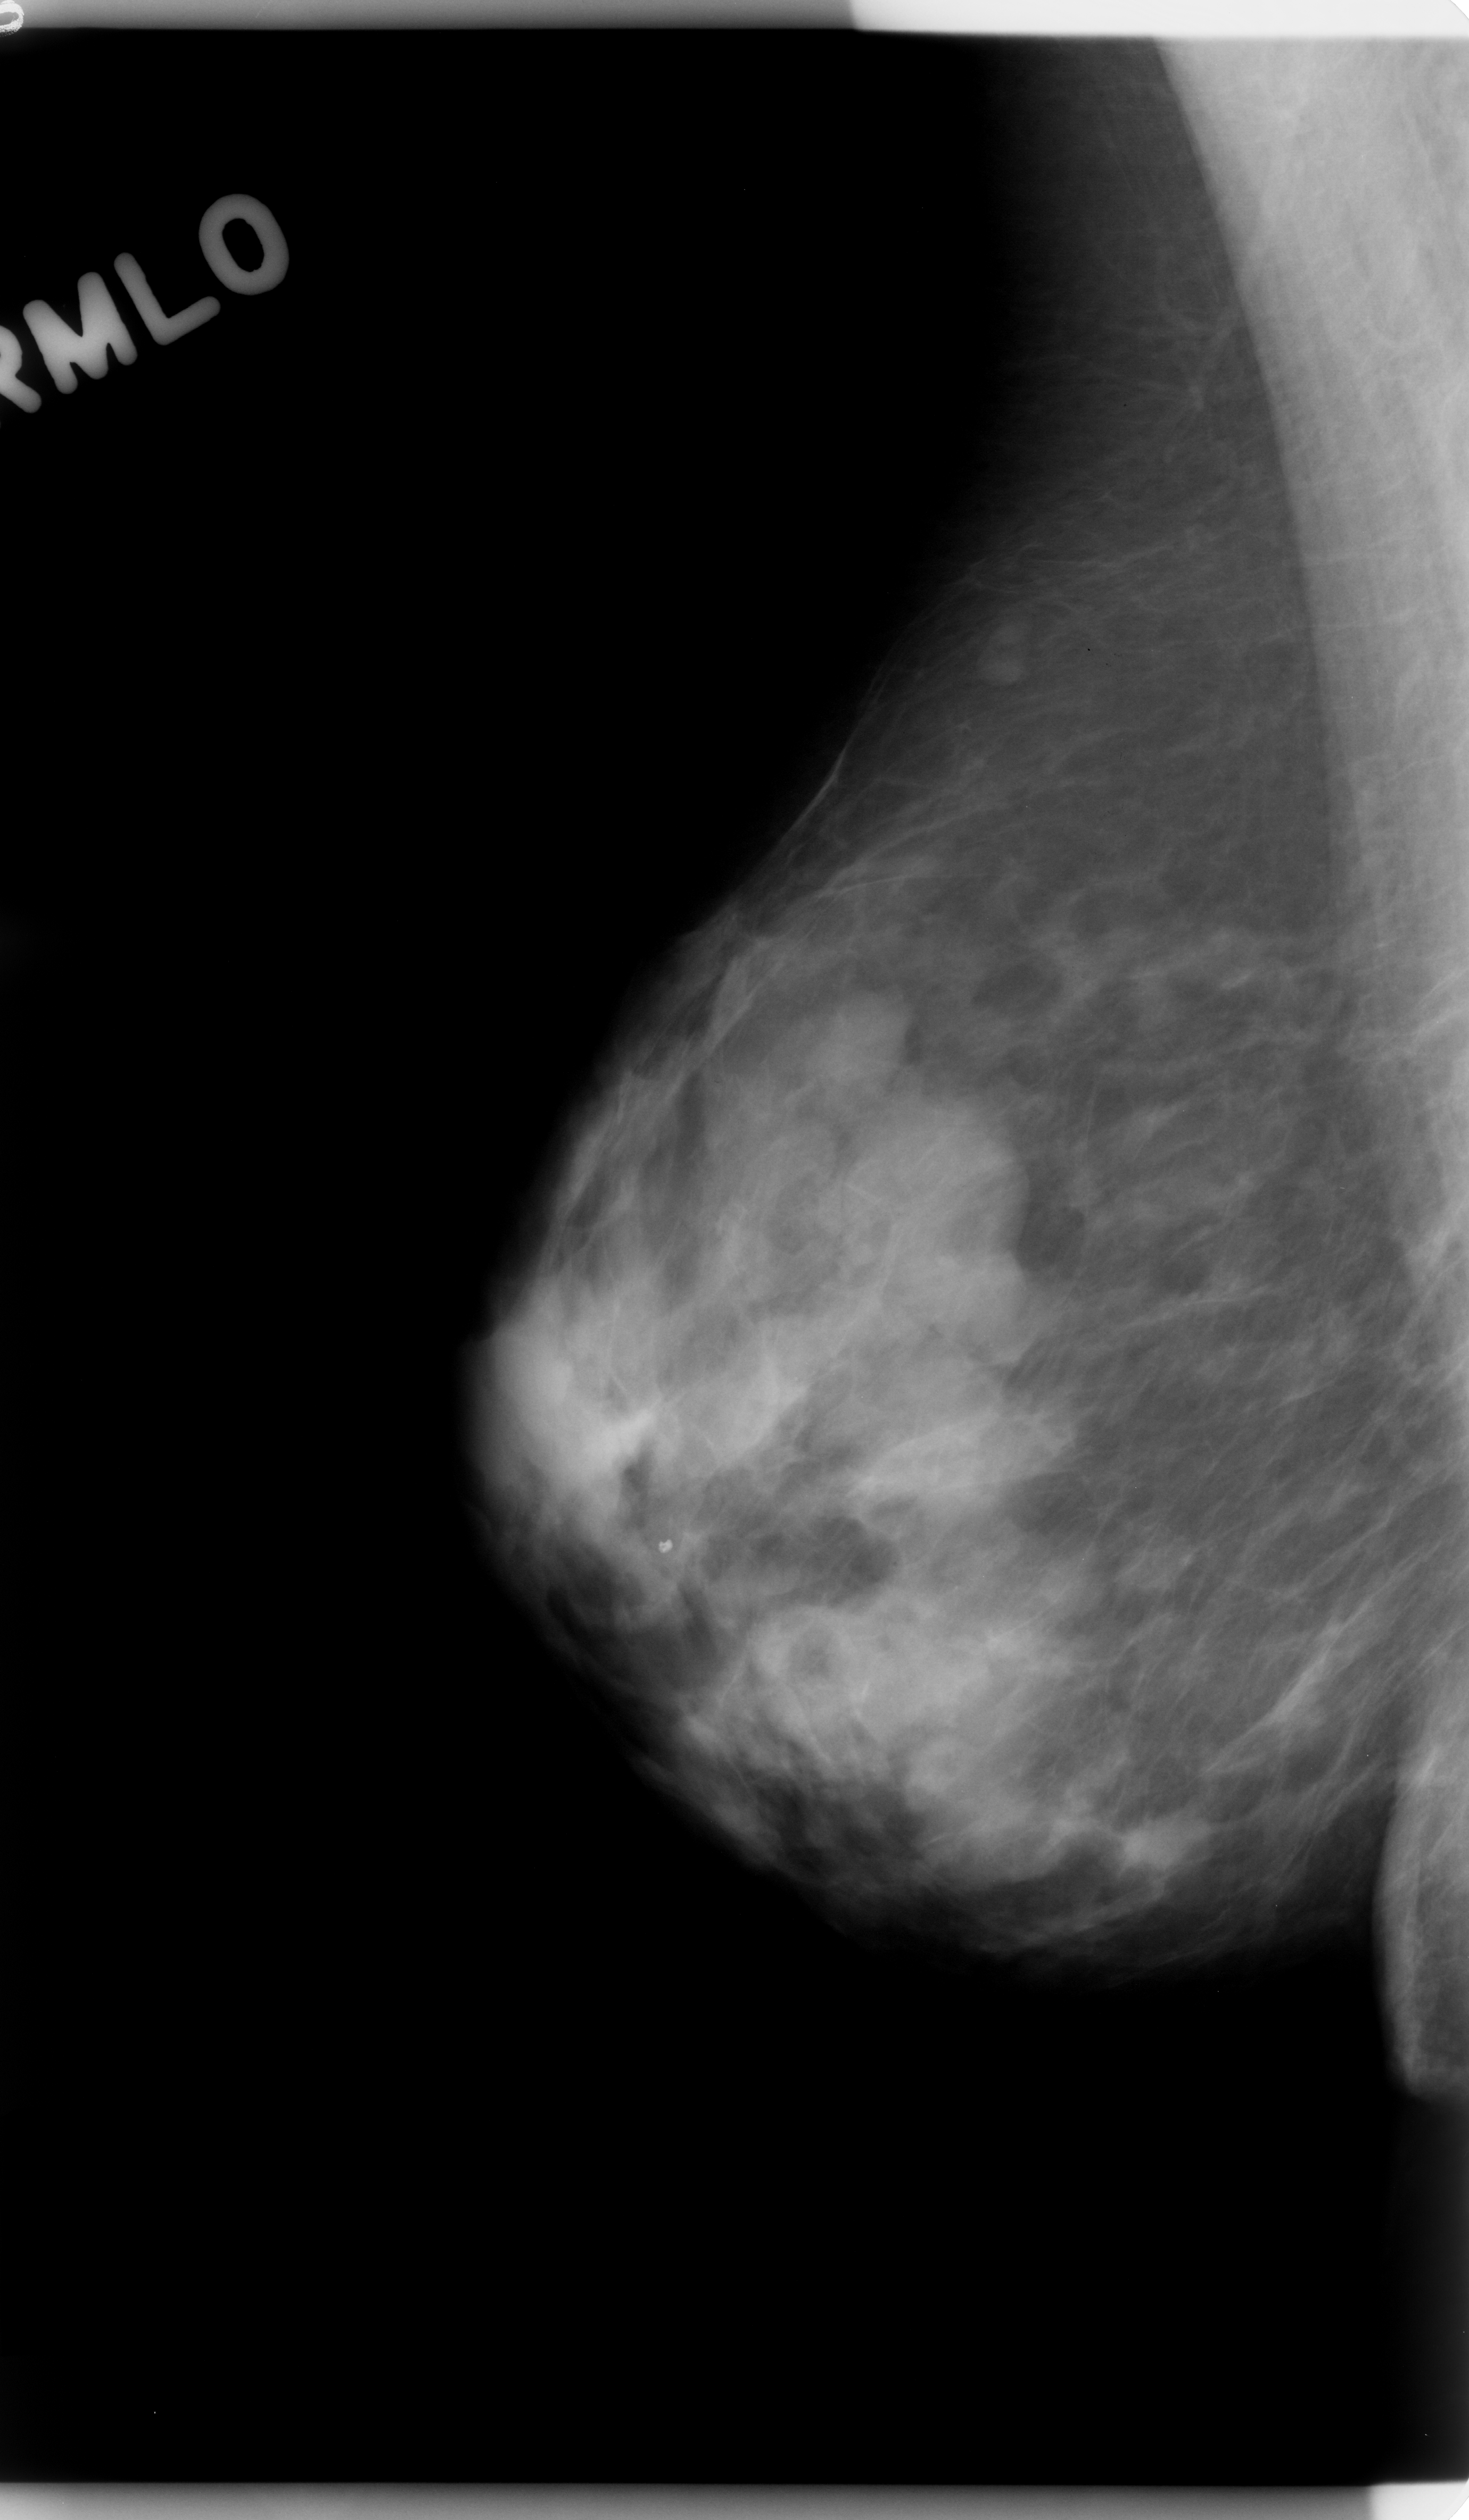
Digitized screen-film mammogram. Right breast. MLO view. BI-RADS breast density category 3 (scale 1–4). 1469 × 2520 image matrix.
Marked abnormalities (boxes around the expert regions of interest):
- mass, shape lobulated, margins circumscribed; BI-RADS assessment category 3; subtlety rating 4 on a 1 (subtle) to 5 (obvious) scale; pathology result (as recorded, not read from the image): benign: bounding box <809,1069,1047,1367> (left, top, right, bottom; pixels)